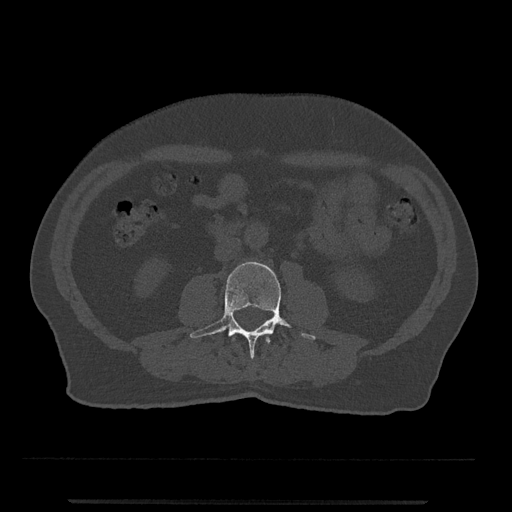
CT including the spine, one axial slice; slice 203 of 797 in the series (ordered by position); 120 kVp; bone window (W 1800 / L 400 HU); 0.5 mm slice thickness; 512 × 512 image matrix, field of view 419 × 419 mm. Male patient, age 63 years. From the clinical record (not read from this slice): primary cancer: prostate.
Annotated regions visible in this slice (semi-automatic segmentation, software-assisted and operator-edited):
- L2 vertebra: box from (x=233, y=337) to (x=270, y=344) px
- L3 vertebra: (x=190, y=262)–(x=316, y=359)